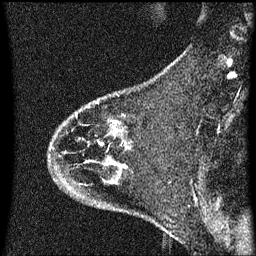
Breast MRI (dynamic contrast-enhanced), one sagittal slice; position 18 of 60 along the scan axis; dynamic contrast-enhanced series, image 2 of 3 at this slice position (ordered by acquisition); 1.5 T; TE 4.2 ms, TR 8.4 ms; 256 × 256 image matrix, field of view 200 × 200 mm. Female patient, age 35 years. Case-level facts recorded for this patient, not image findings: setting: breast cancer imaged before/during neoadjuvant chemotherapy; receptor status: HER2-positive.
Structures marked on this image (semi-automatically segmented with operator editing):
- analysis volume of interest (the breast-tissue region the enhancement analysis was run in; not a lesion): bounding box [x1, y1, x2, y2] px = [48, 68, 173, 173]
- tumour enhancement mask (voxels above the 70 % enhancement threshold inside the analysis volume of interest): [114, 122, 116, 125]